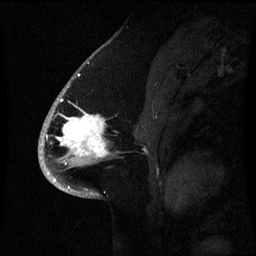
Breast MRI (dynamic contrast-enhanced), one sagittal slice; position 38 of 60 along the scan axis; dynamic contrast-enhanced series, image 2 of 3 at this slice position (ordered by acquisition); 1.5 T; TE 4.2 ms, TR 8.4 ms; 2.1 mm slice thickness; 256 × 256 image matrix. Female patient, age 53 years. Case-level facts recorded for this patient, not image findings: setting: breast cancer imaged before/during neoadjuvant chemotherapy; receptor status: HR-positive, HER2-negative.
Structures marked on this image (semi-automatic segmentation, software-assisted and operator-edited):
- analysis volume of interest (the breast-tissue region the enhancement analysis was run in; not a lesion): box from (x=52, y=90) to (x=116, y=171) px
- tumour enhancement mask (voxels above the 70 % enhancement threshold inside the analysis volume of interest): (x=57, y=112)–(x=109, y=165)